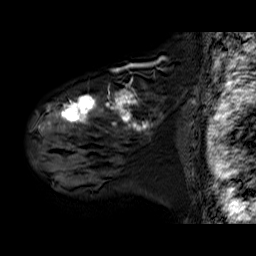
Breast MRI (dynamic contrast-enhanced), one sagittal slice; slice 48 of 60 in the series (ordered by position); dynamic contrast-enhanced series, time point 2 of 6 at this slice position (early post-contrast); 1.5 T; TE 6.3 ms, TR 32.9 ms; 256 × 256 image matrix, field of view 200 × 200 mm. Female patient. Case-level facts recorded for this patient, not image findings: setting: breast cancer imaged before/during neoadjuvant chemotherapy; receptor status: HER2-positive.
Structures marked on this image (semi-automatic segmentation, software-assisted and operator-edited):
- analysis volume of interest (the breast-tissue region the enhancement analysis was run in; not a lesion): box from (x=31, y=81) to (x=182, y=180) px
- tumour enhancement mask (voxels above the 100 % enhancement threshold inside the analysis volume of interest): (x=39, y=93)–(x=152, y=134)